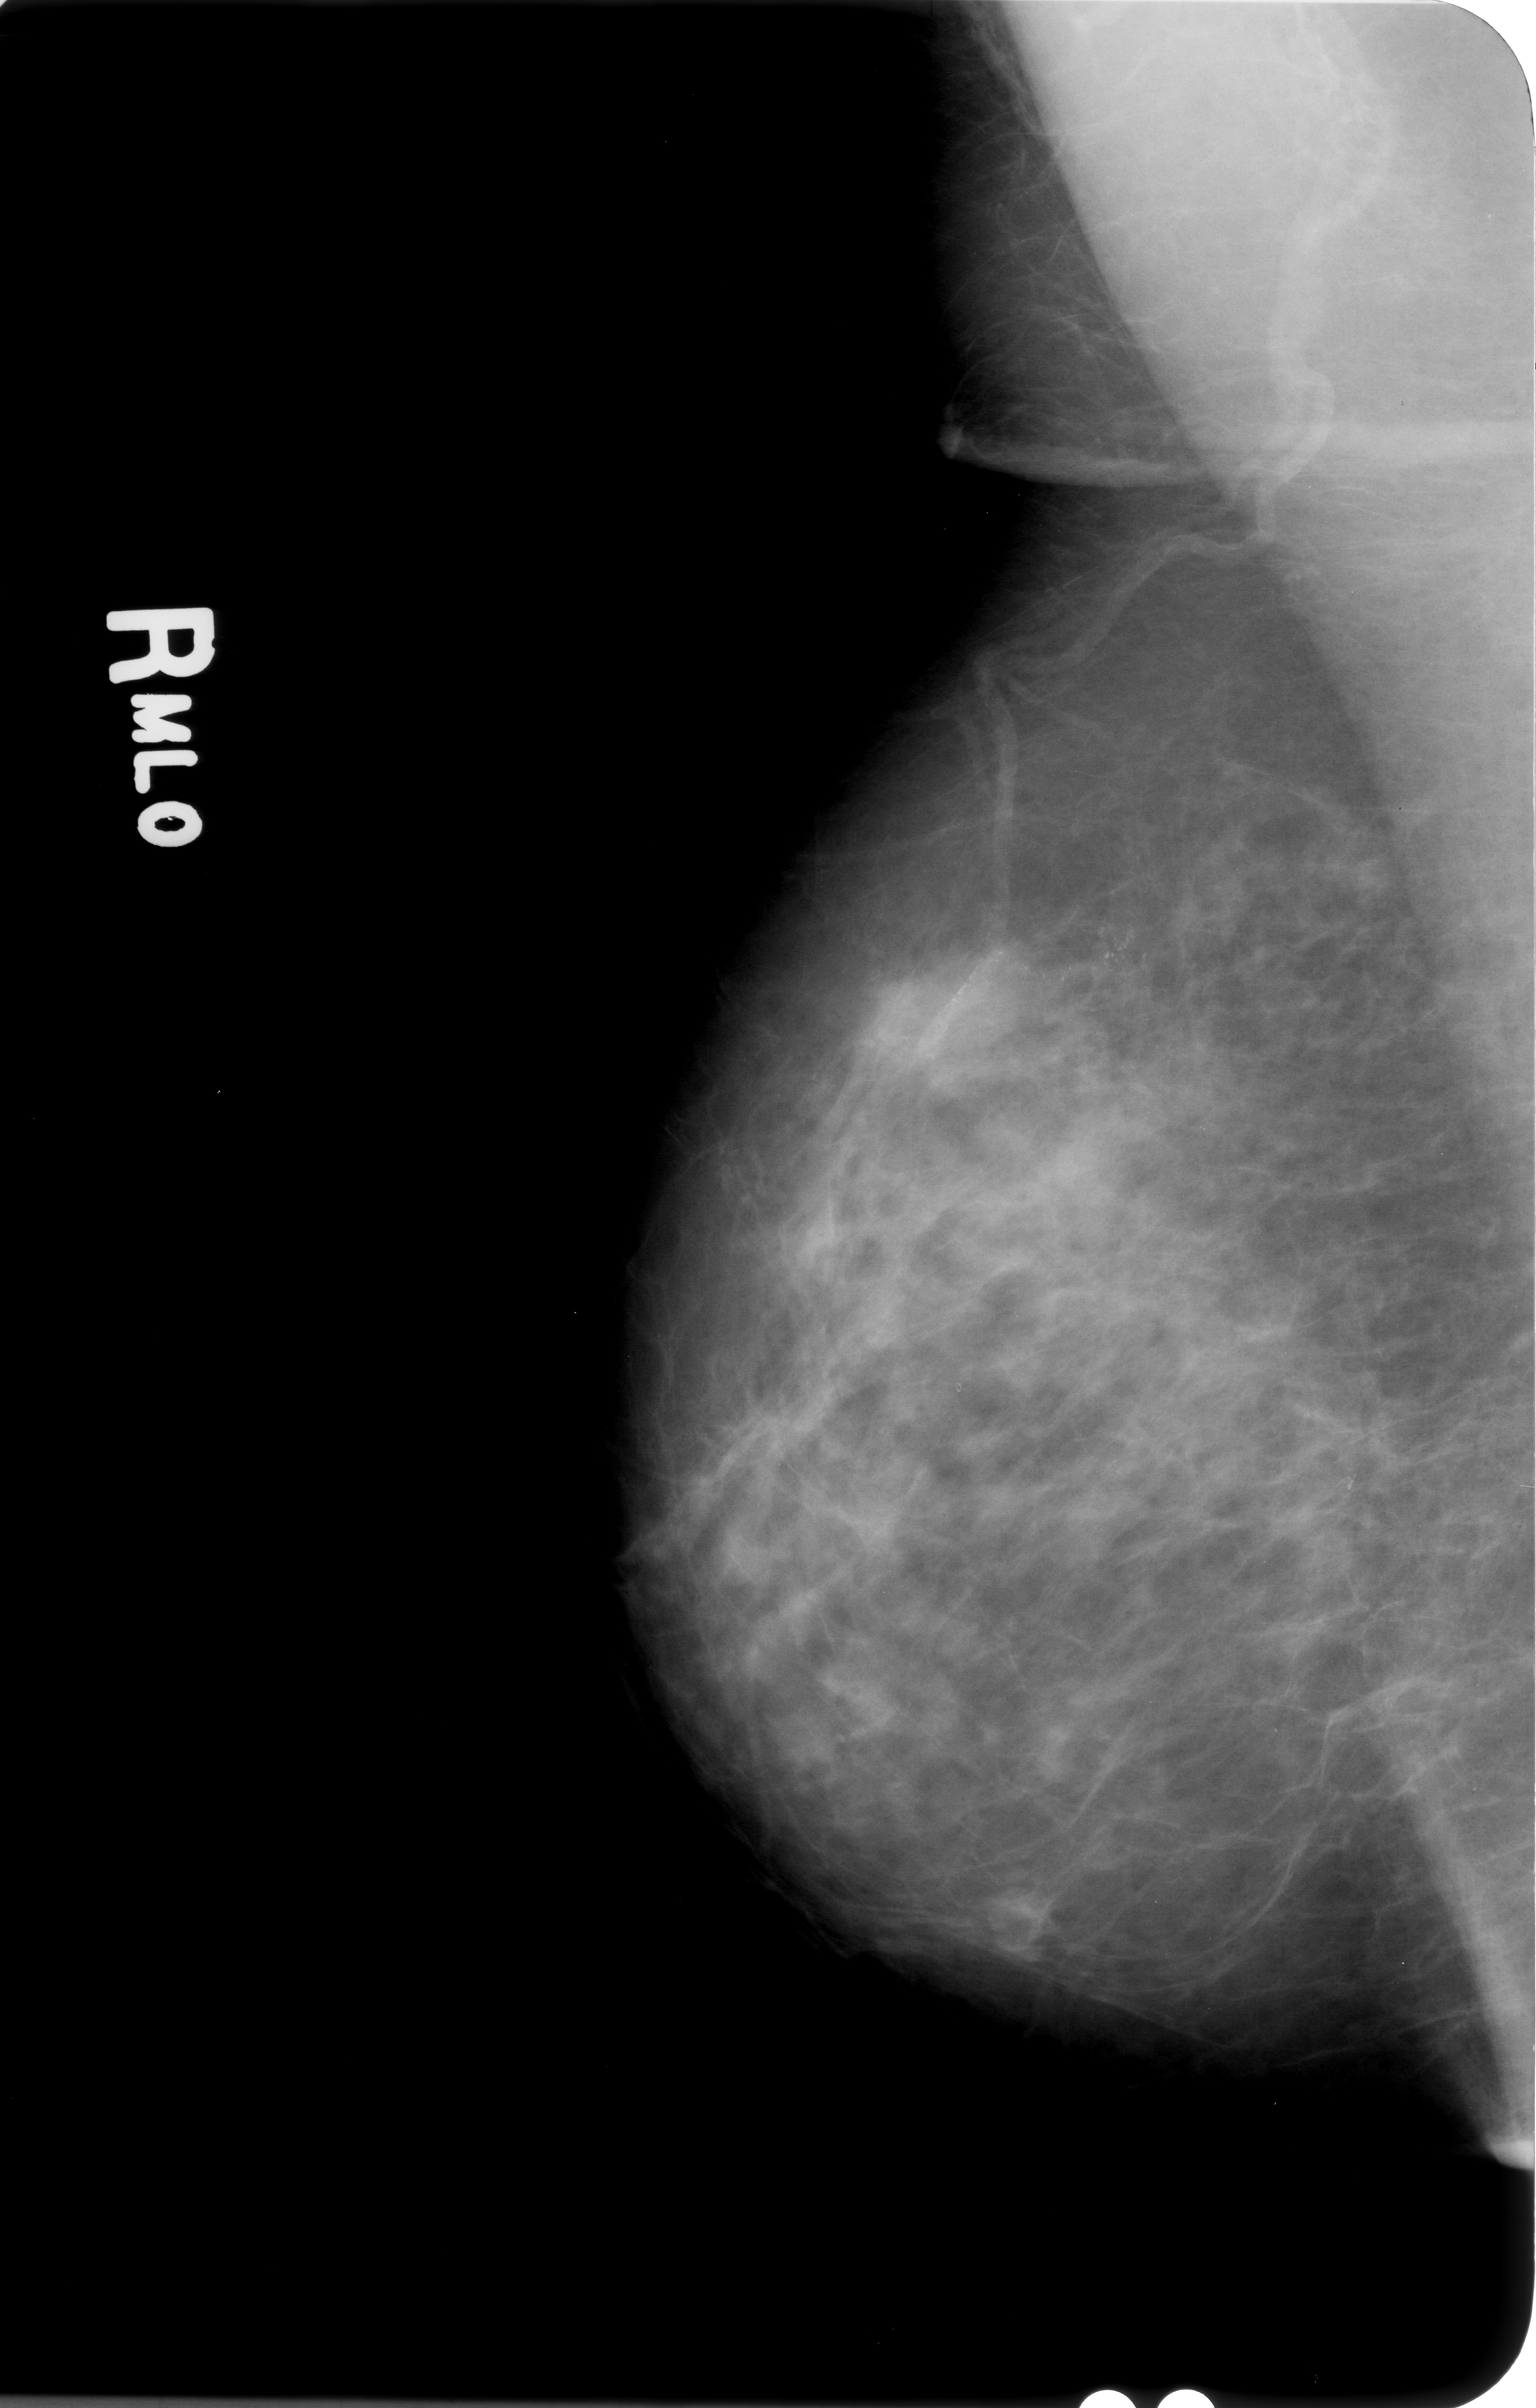
Scanned film-screen mammogram. Right breast. Mediolateral oblique (MLO) view. Breast composition: heterogeneously dense (BI-RADS density category 3 of 4). 1536 × 2408 image matrix.
Expert-marked regions of interest on this image (one box per marked abnormality):
- calcifications, morphology pleomorphic, distribution clustered / linear; BI-RADS assessment category 4; subtlety rating 3 on a 1 (subtle) to 5 (obvious) scale; pathology (as recorded): benign: bounding box (x1, y1, x2, y2) in pixels: (981, 904, 1167, 998)